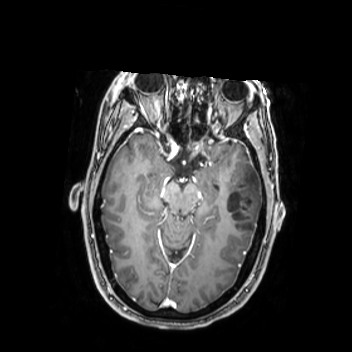
Brain MRI from a brain-tumour surgery series, one axial slice. Position 160 of 350 along the scan axis. T1-weighted post-contrast. 352 × 352 image matrix. From the clinical record (not read from this slice): histopathology: Oligodendroglioma; WHO grade: 2; IDH mutation: yes; tumour location: Left Middle Temporal Gyrus.
Structures marked on this image (outlined manually by an expert reader):
- tumour: bounding box [x1, y1, x2, y2] px = [224, 163, 262, 236]